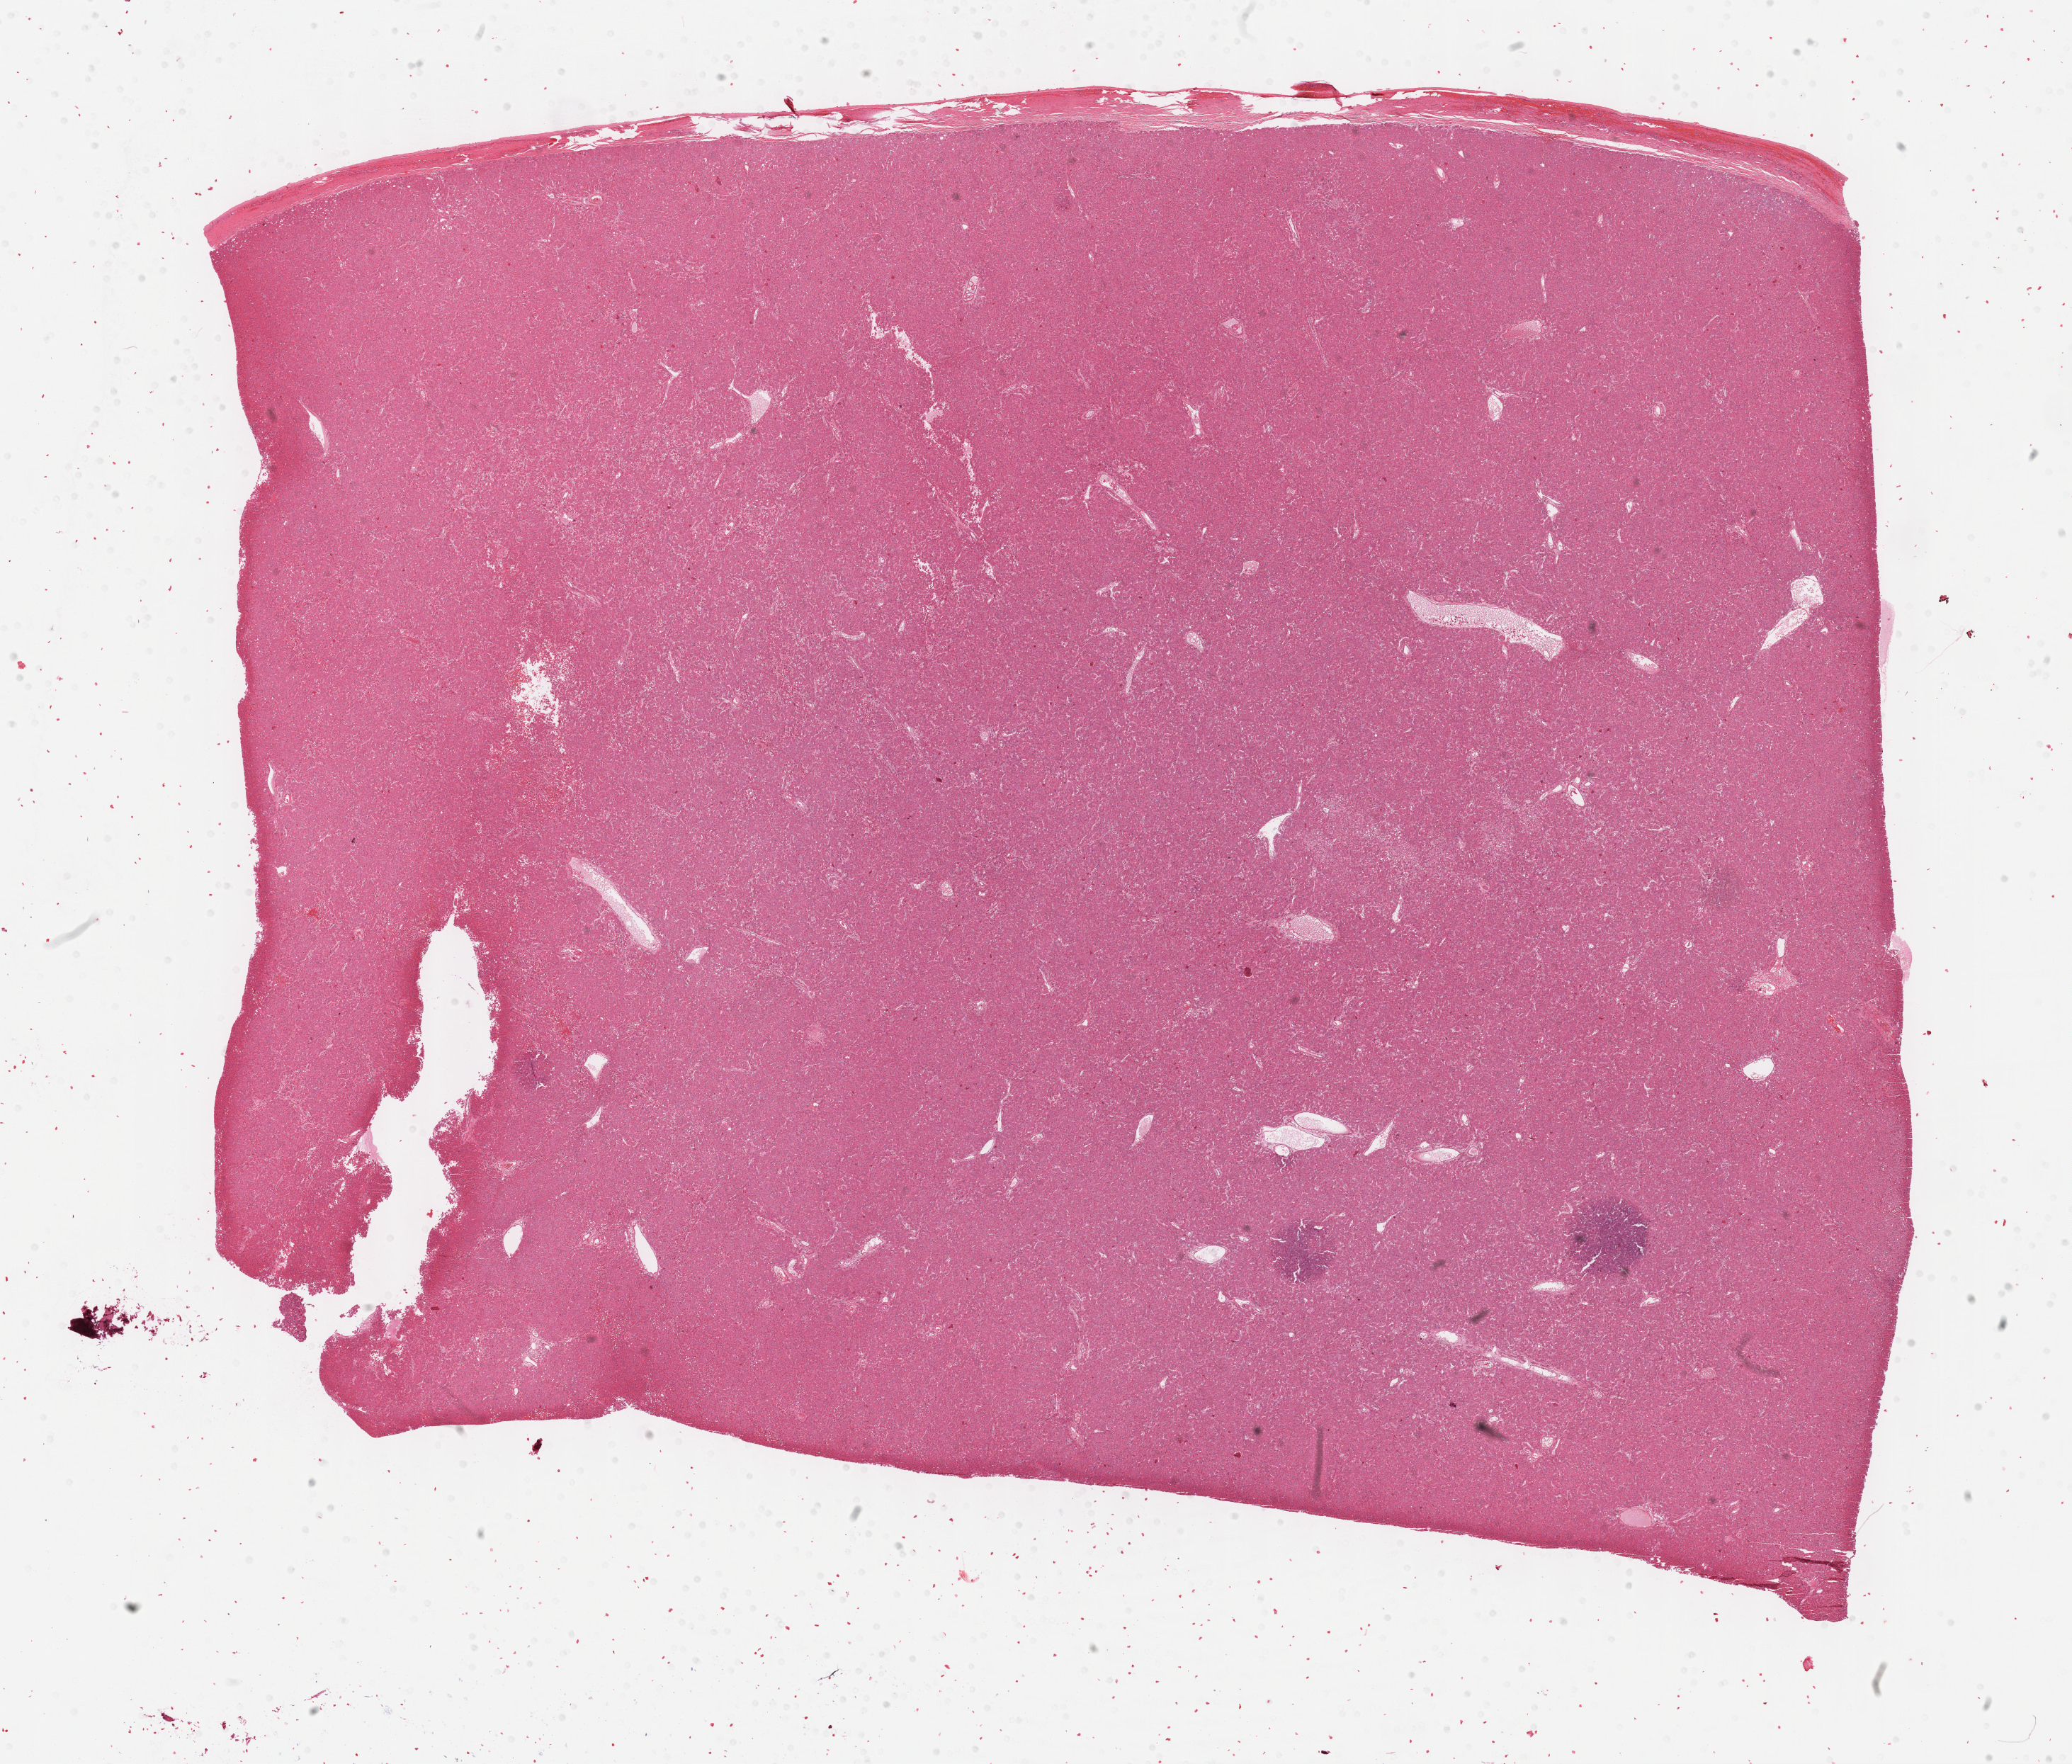
Digitized H&E-stained tissue section (whole slide), whole scanned area (about 23.7 x 20.1 mm) shown as a low-resolution overview, formalin-fixed paraffin-embedded (FFPE) diagnostic section, liver, primary tumour sample. Female patient; age at initial diagnosis 67 years.
Diagnosis: Hepatocellular carcinoma, NOS.